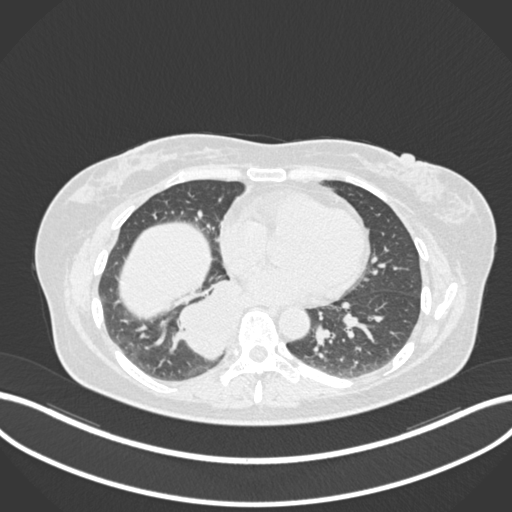
Chest CT, one axial slice. Slice 561 of 677 in the series (ordered by position). 120 kVp. Lung window (W 1500 / L -600 HU). 1 mm slice thickness. 512 × 512 image matrix, field of view 400 × 400 mm. Patient: female, 54 years. From the clinical record (not read from this slice): clinical TNM (as recorded): T4 N0 M0.
Outlined on this slice (bounding box drawn by a radiologist):
- lung tumour (recorded histology: adenocarcinoma): box from (x=170, y=281) to (x=247, y=360) px